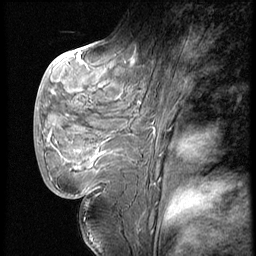
Breast MRI (dynamic contrast-enhanced), one sagittal slice; slice 24 of 62 in the series (ordered by position); dynamic contrast-enhanced series, image 2 of 4 at this slice position (ordered by acquisition); 1.5 T; TE 4.2 ms, TR 9 ms; 2.5 mm slice thickness; 256 × 256 image matrix, field of view 180 × 180 mm. Patient: female, 28 years. Case-level facts recorded for this patient, not image findings: setting: breast cancer imaged before/during neoadjuvant chemotherapy.
Structures marked on this image (semi-automatically segmented with operator editing):
- analysis volume of interest (the breast-tissue region the enhancement analysis was run in; not a lesion): bounding box (x1, y1, x2, y2) in pixels: (41, 54, 150, 183)
- tumour enhancement mask (voxels above the 140 % enhancement threshold inside the analysis volume of interest): (77, 151, 104, 170)